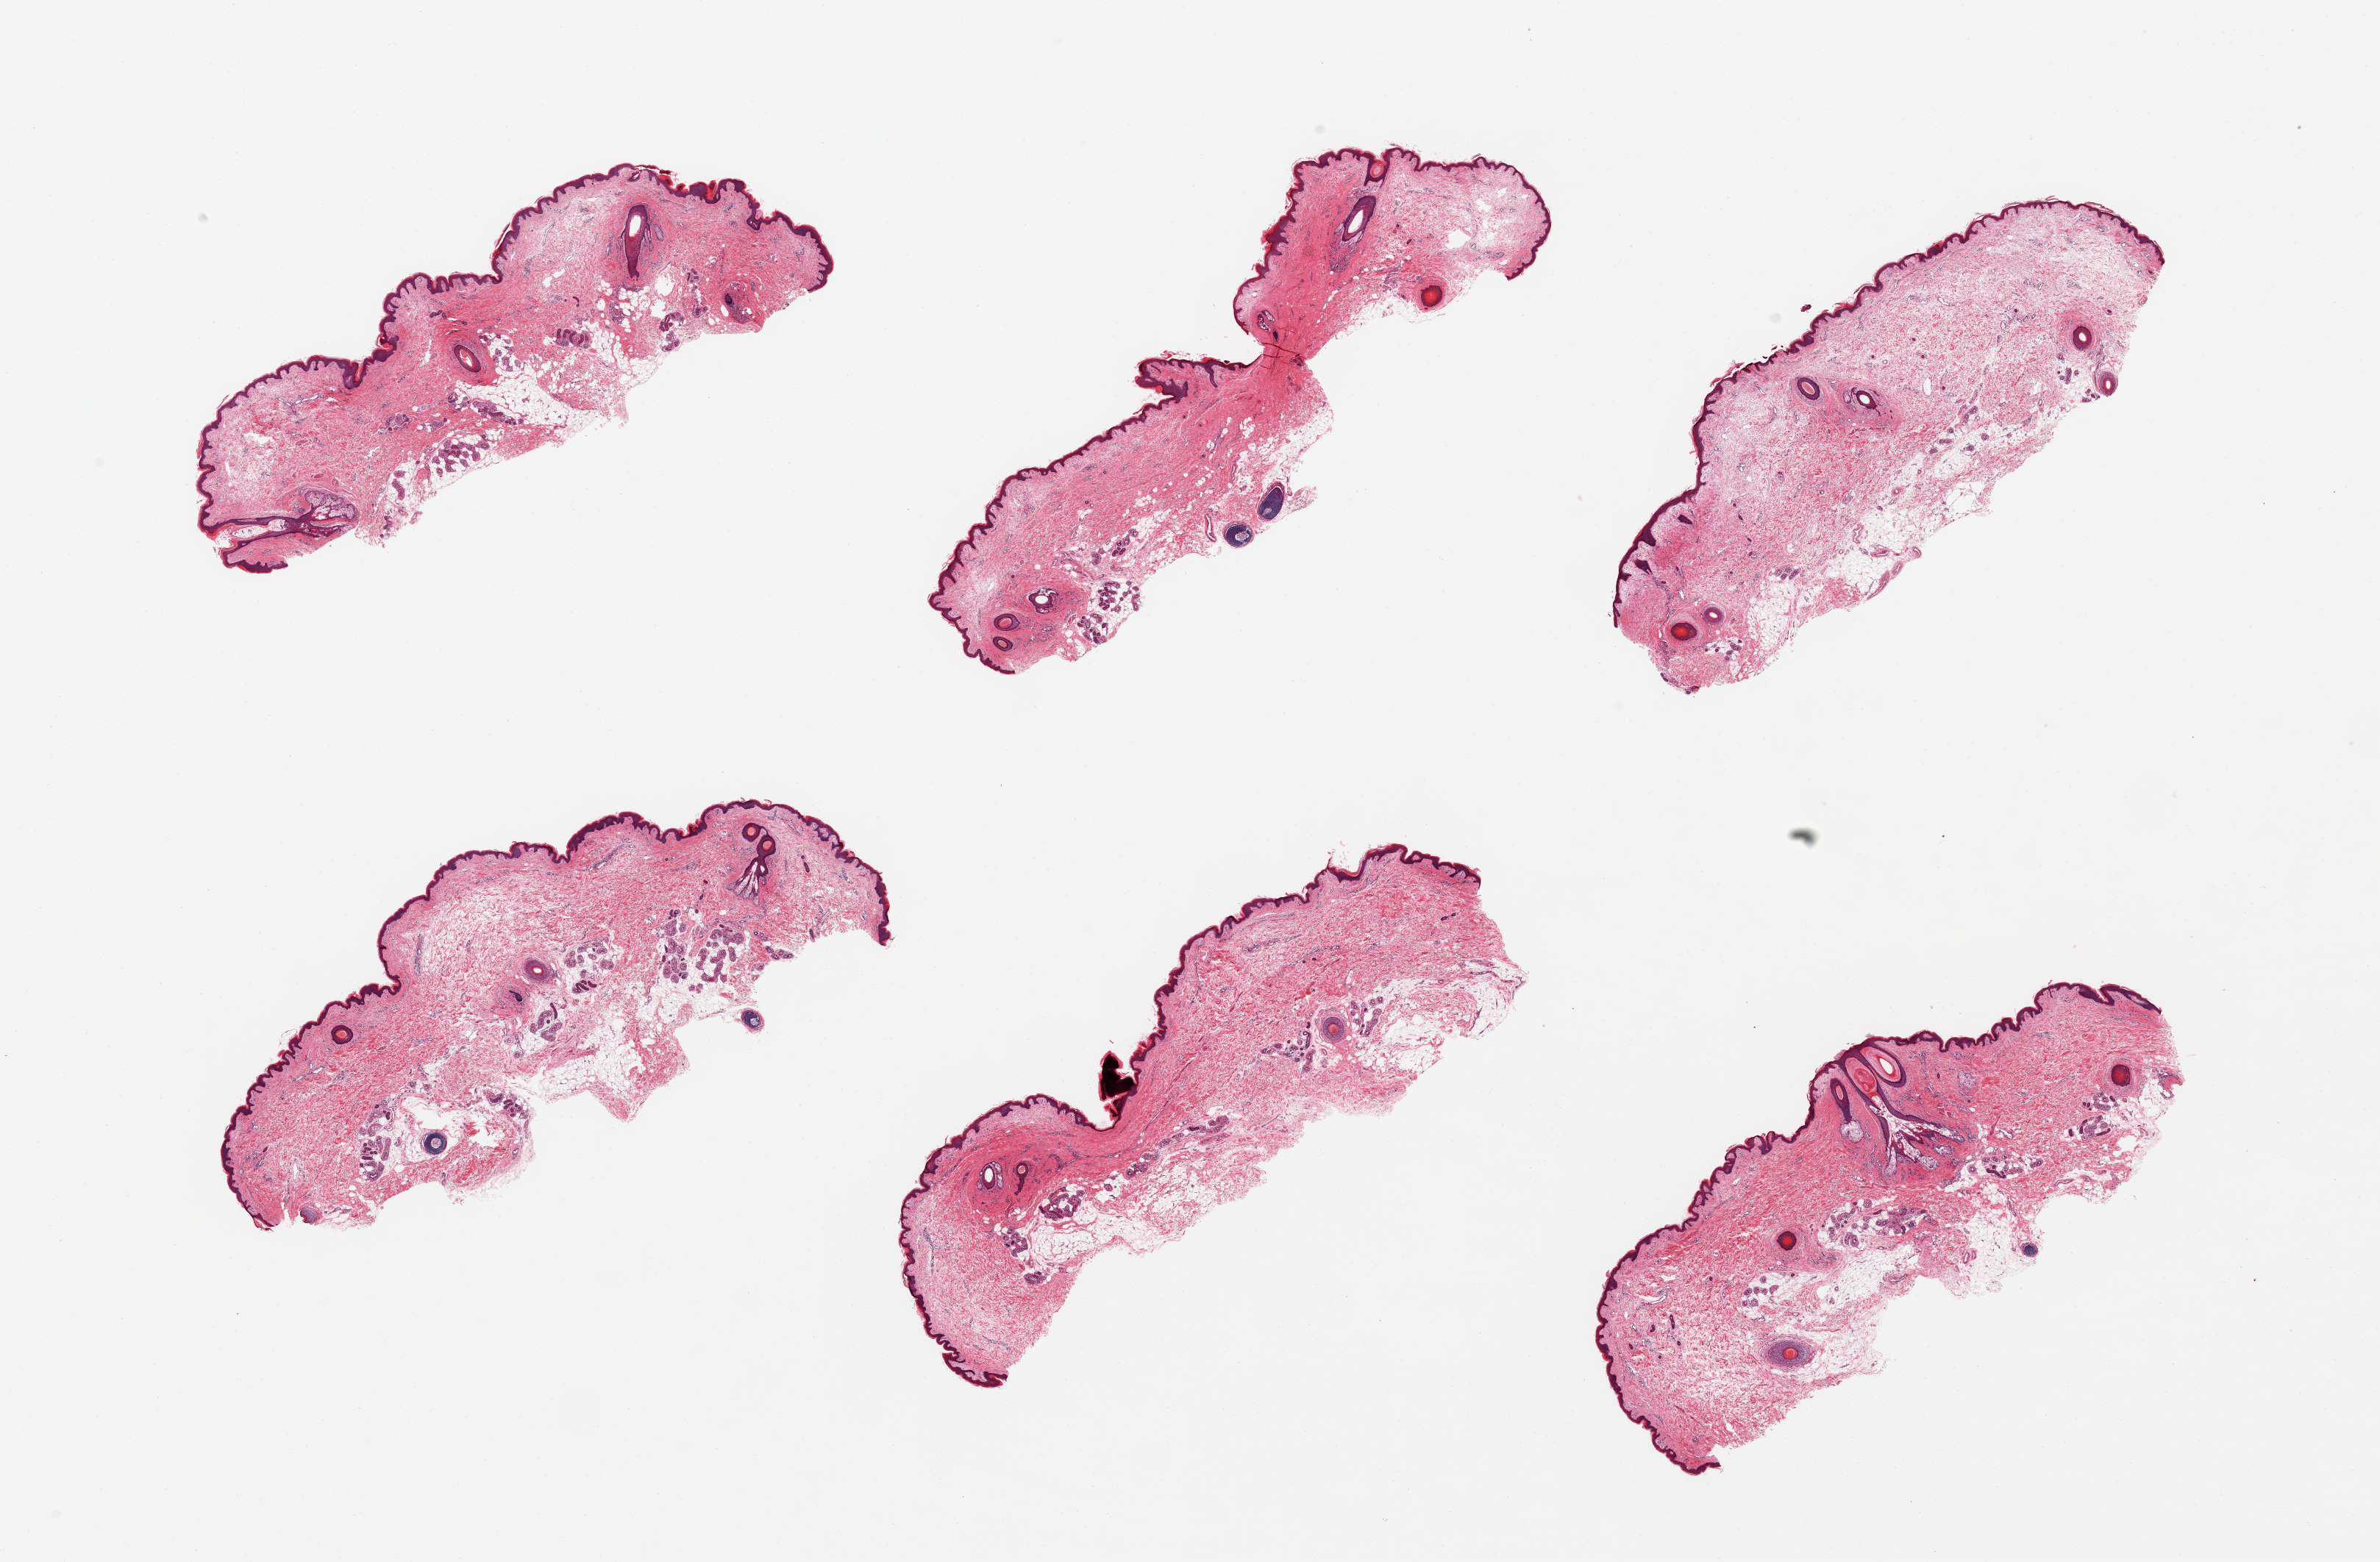
Digitized H&E-stained section, brightfield — low-resolution overview of the scanned area, about 25.6 x 16.8 mm. PAXgene-fixed paraffin-embedded (PFPE) section. Section of skin of suprapubic region (target tissue). Donor tissue sample. Donor sex: female.
• review note (as recorded): 6 pieces; well trimmed; edematous dermis